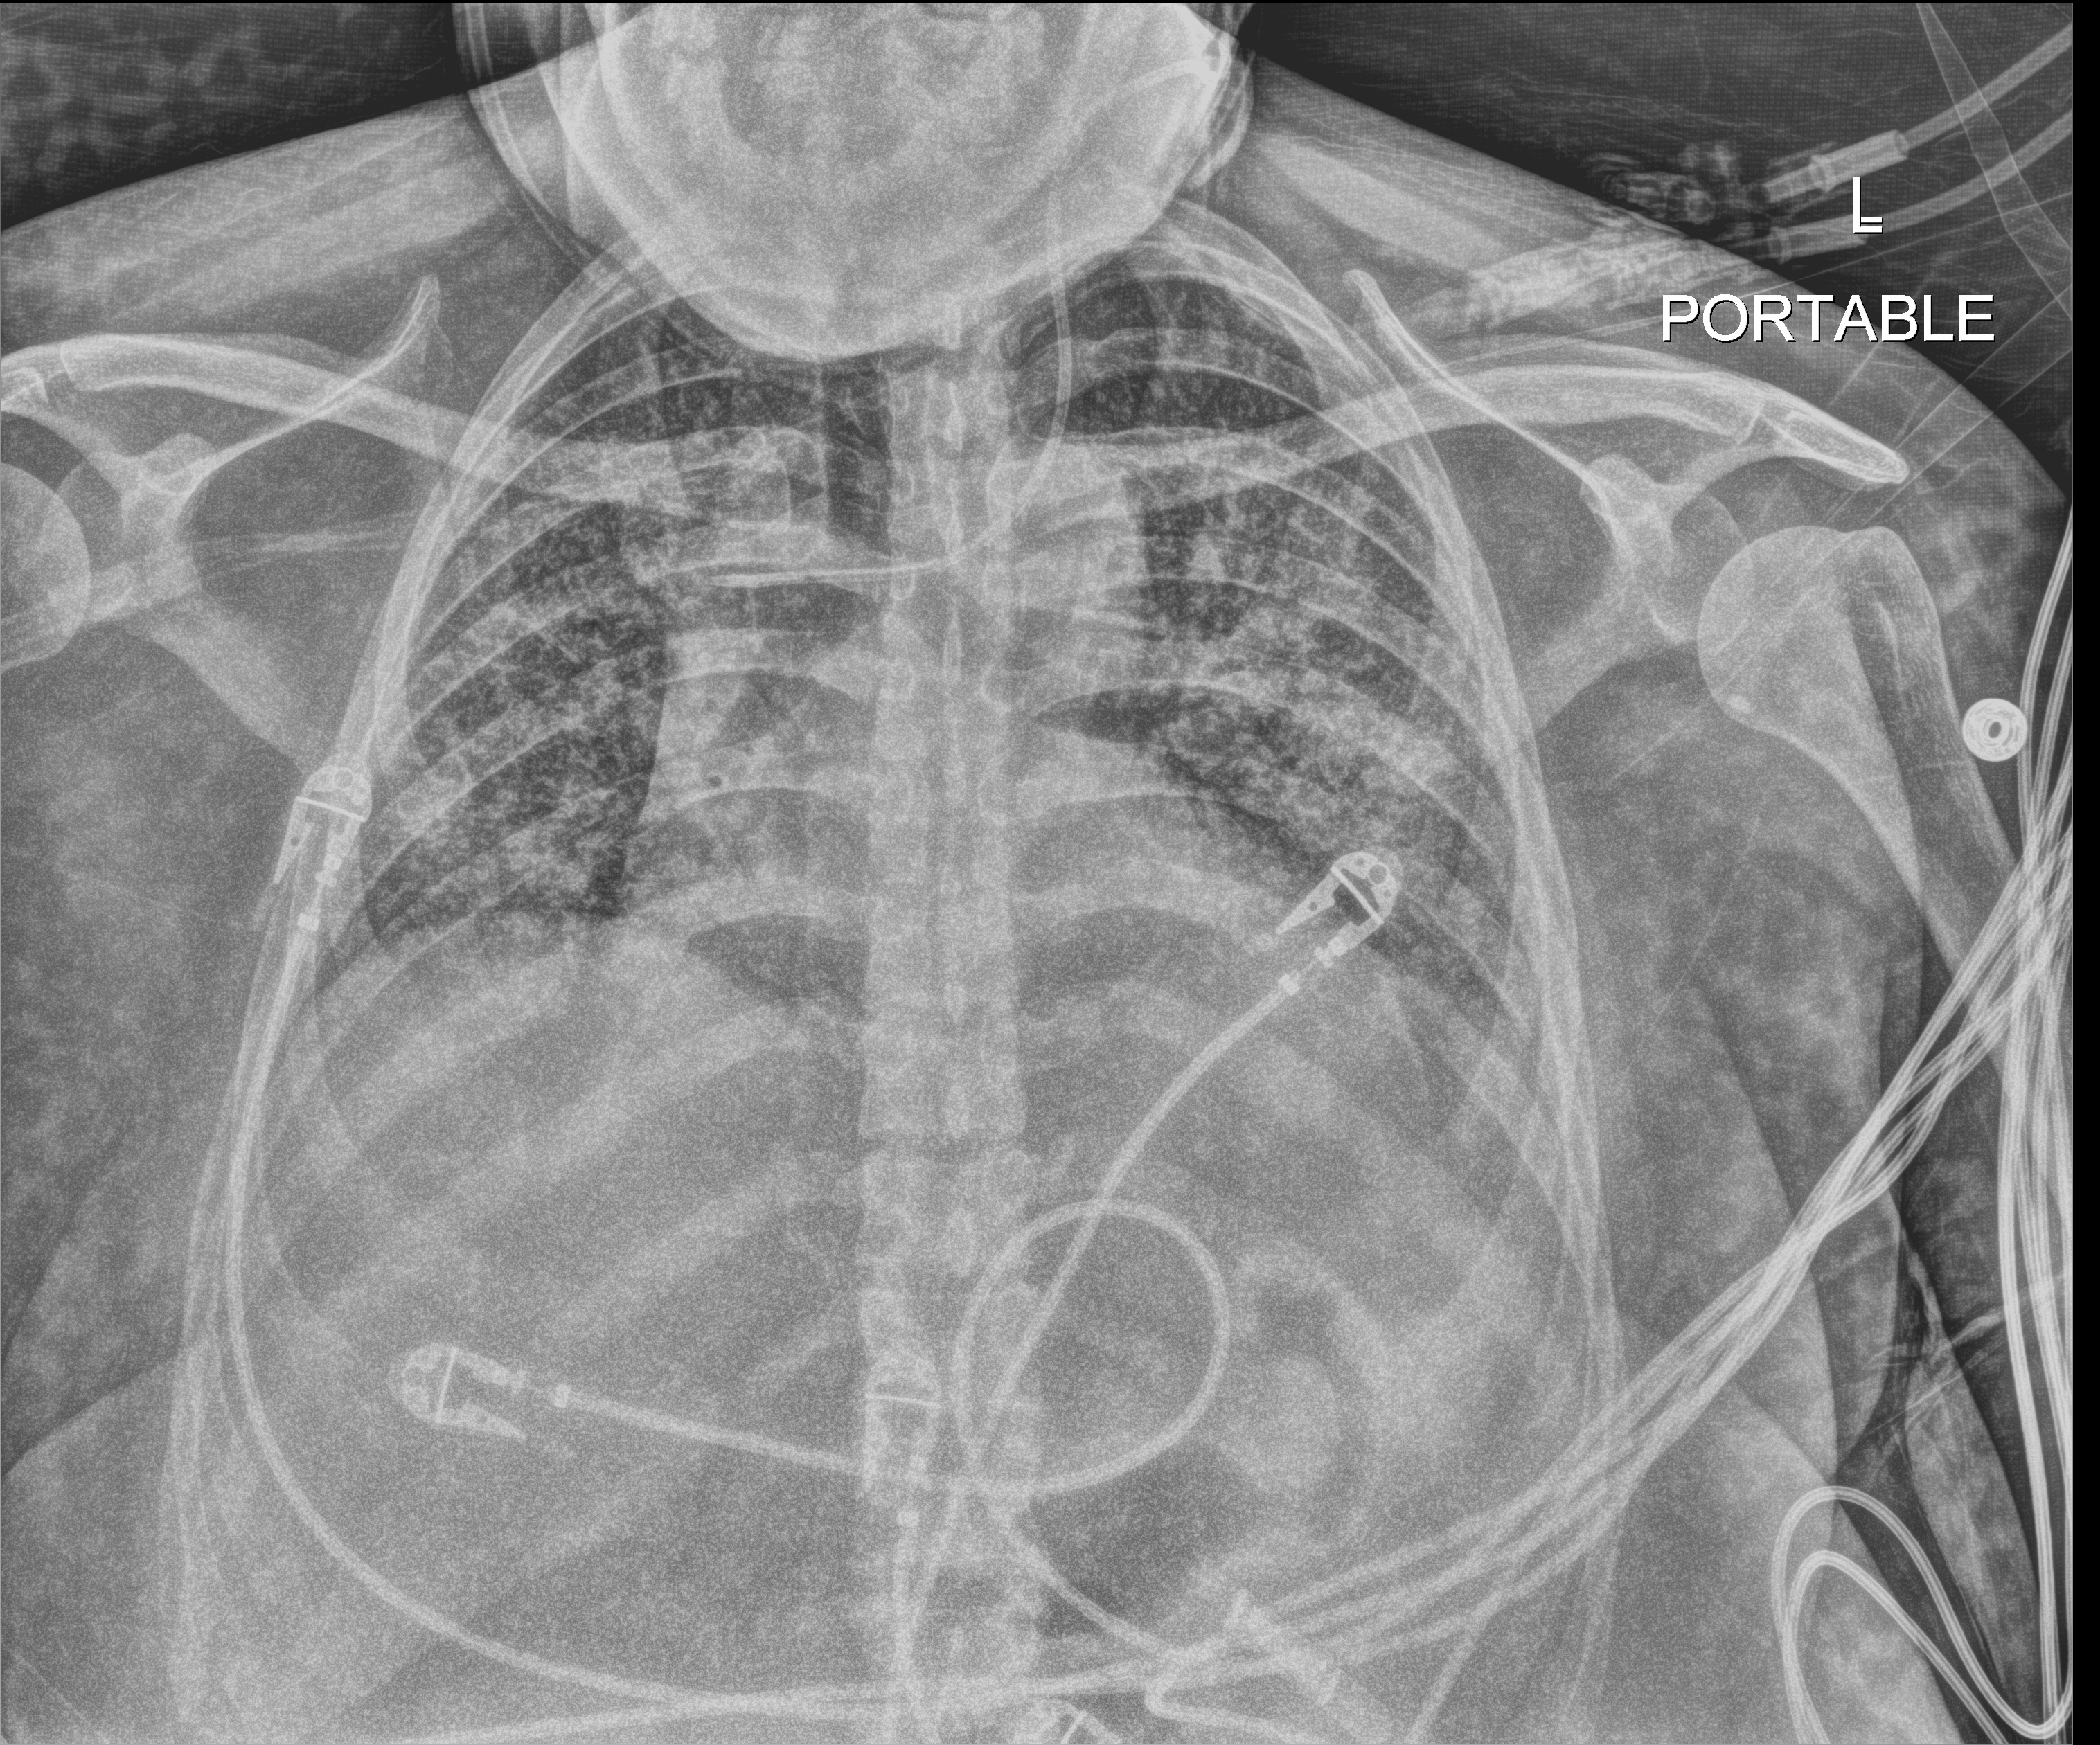
Chest X-ray (portable), anteroposterior (AP) projection. Patient hospitalised with COVID-19; female, aged 18–59 years.
From the hospital-stay record, not from the radiograph (when in the stay this image was taken is not recorded):
- length of hospital stay: 33 days
- admitted to intensive care during this hospital stay: no